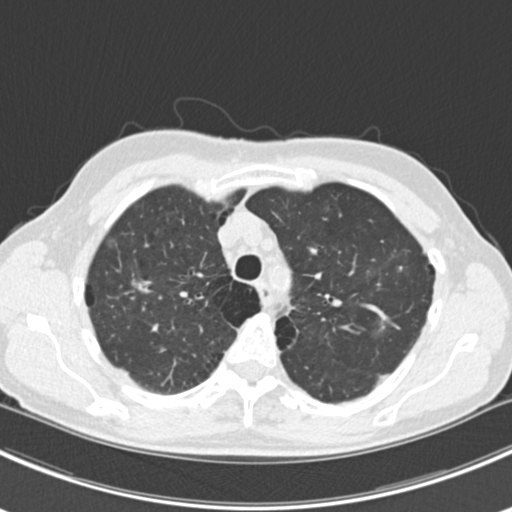
Low-dose screening chest CT, axial slice; baseline screening round; lung window (W 1500 / L -600 HU); 2 mm slice thickness. Female participant, aged 63 years at enrolment.
• Lesion marked by an expert reader, box from (x=363, y=235) to (x=436, y=309) px.
• The screening reader recorded 10 non-calcified nodules or masses ≥4 mm on this exam (right lower lobe, right lower lobe, left lower lobe, left lower lobe, right middle lobe, right lower lobe, left lower lobe, left upper lobe, right upper lobe, left upper lobe); which of them this box marks is not recorded.
• Official screen result: positive, change unspecified: nodule(s) >= 4 mm or enlarging nodule(s), mass(es), or other non-specific abnormalities suspicious for lung cancer.